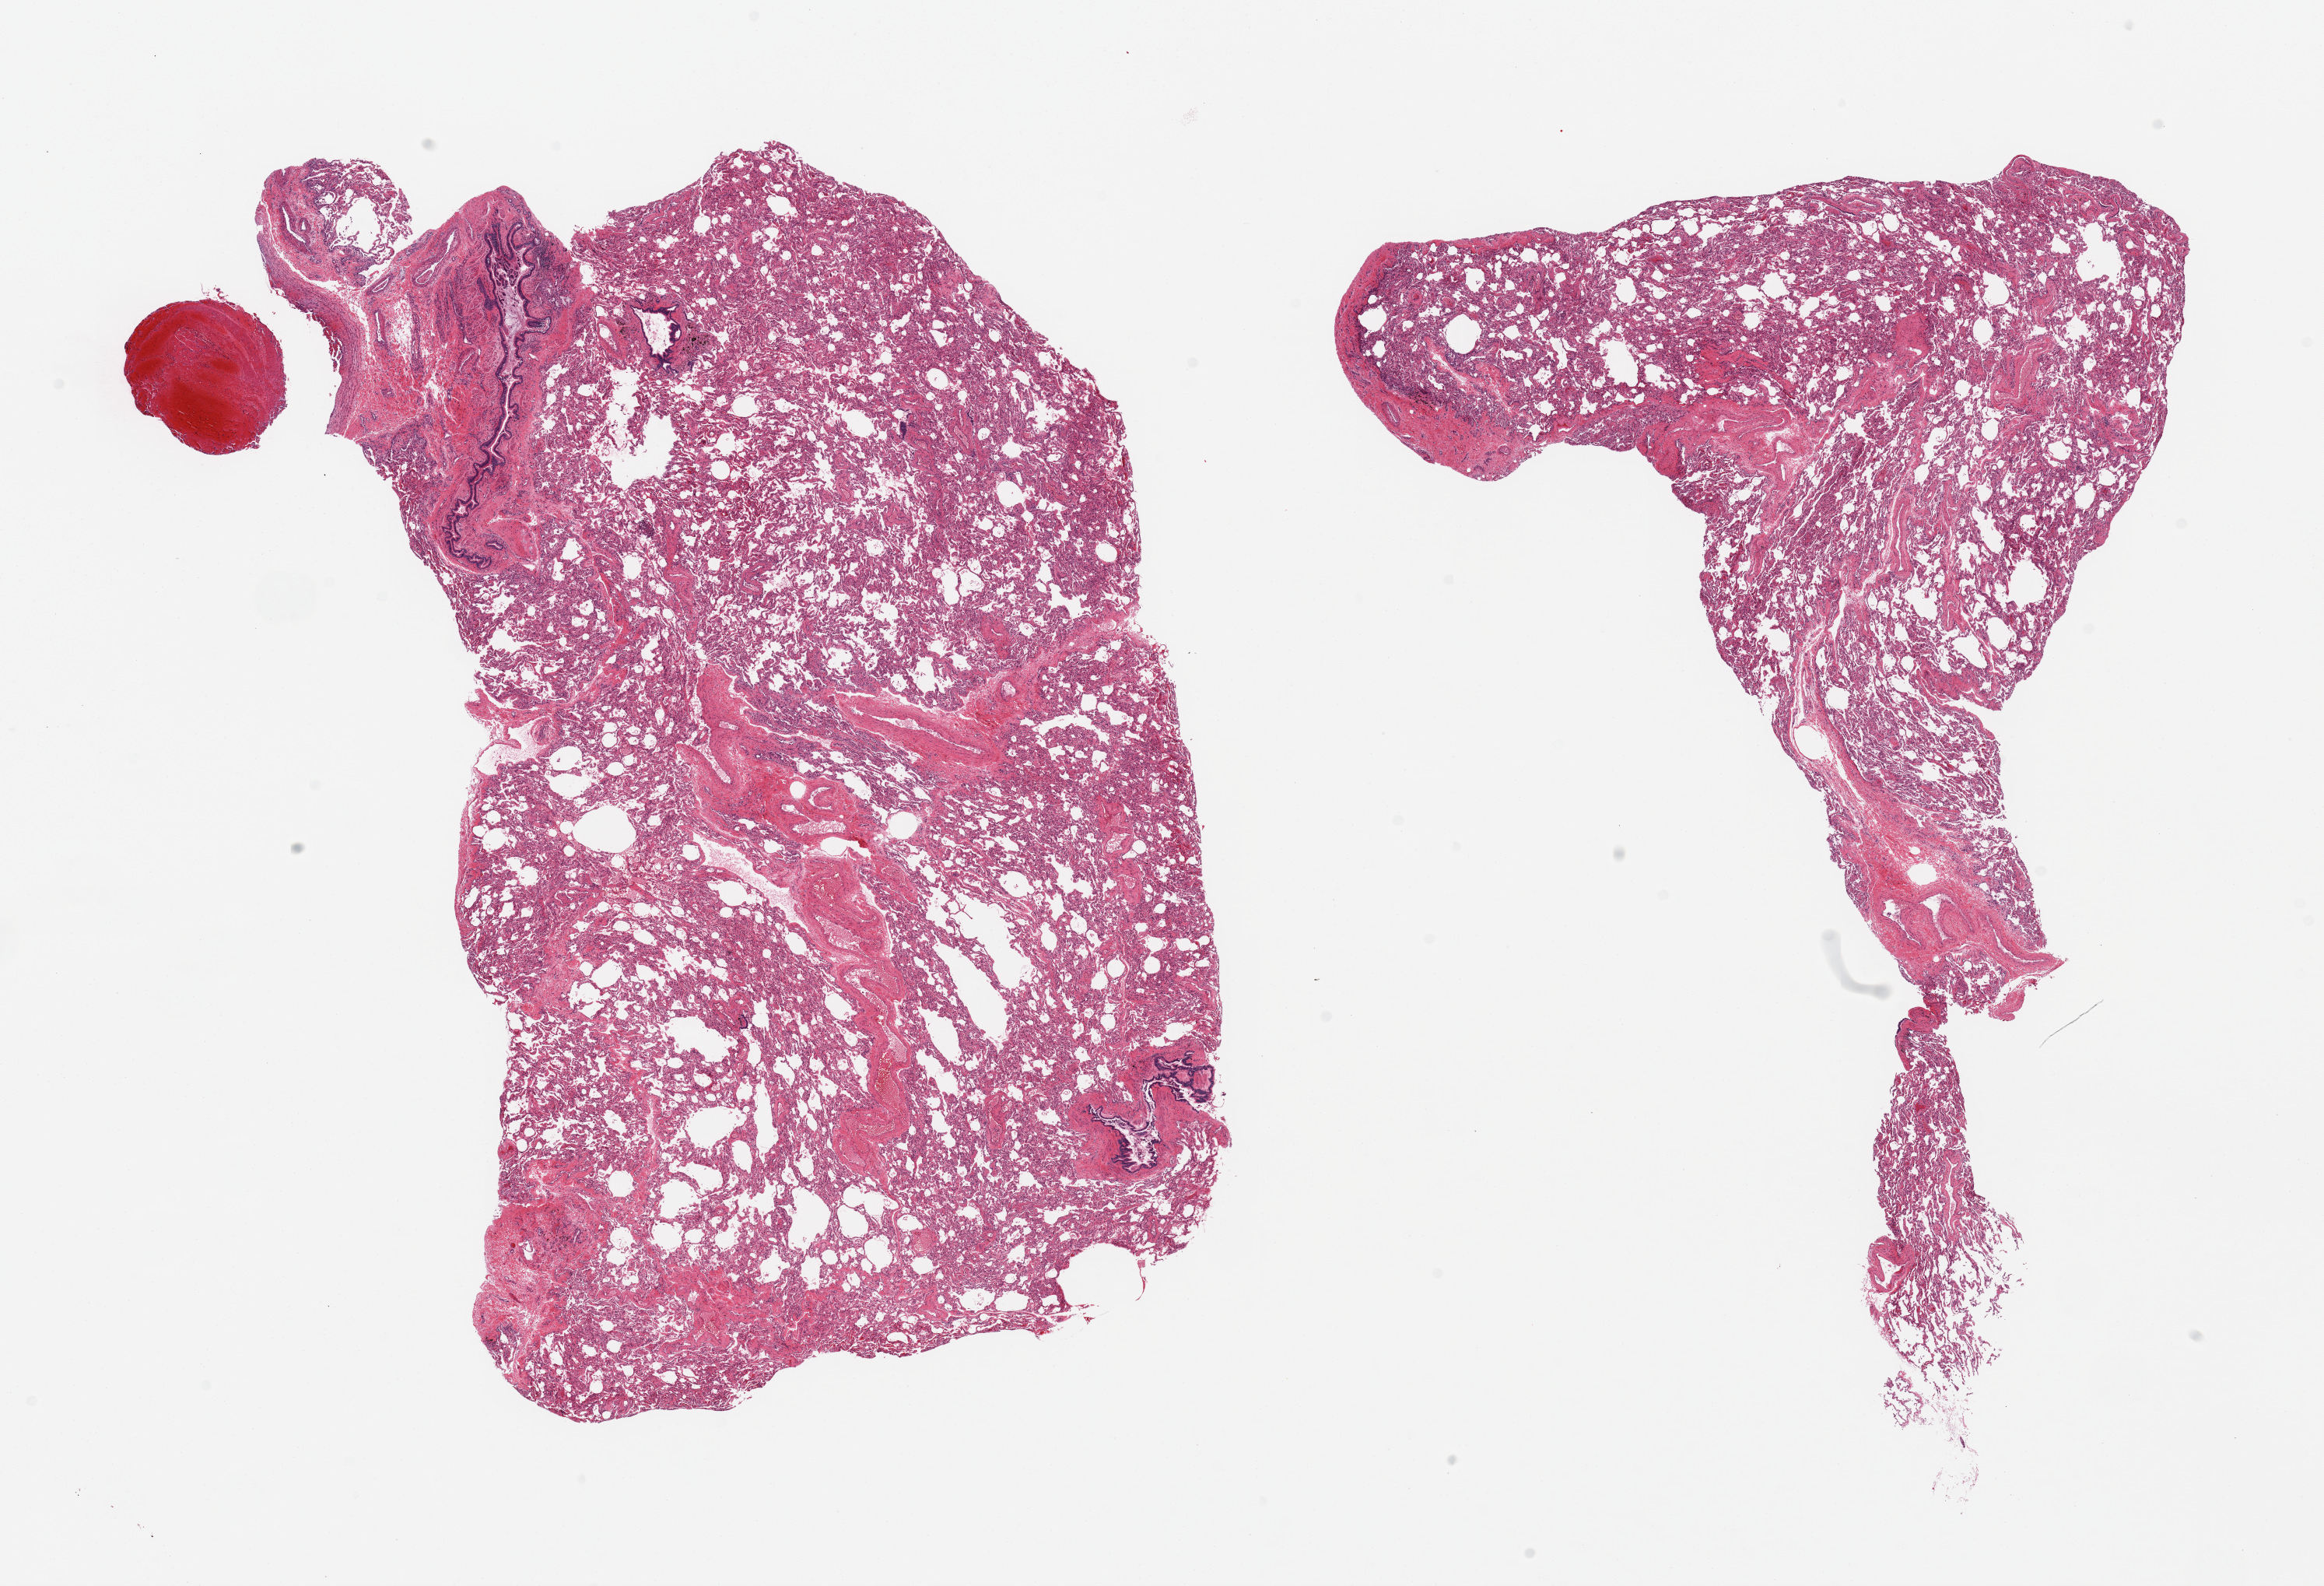
Hematoxylin and eosin (H&E) whole-slide image, brightfield — shown as a low-resolution overview of the whole scanned area (about 23.6 x 16.1 mm). PAXgene-fixed, paraffin-embedded tissue. Target tissue: lung. Donor tissue sample. Donor: female.
Review note (as recorded): 2 pieces; minimal congestion, well-preserved bronchial mucosa.